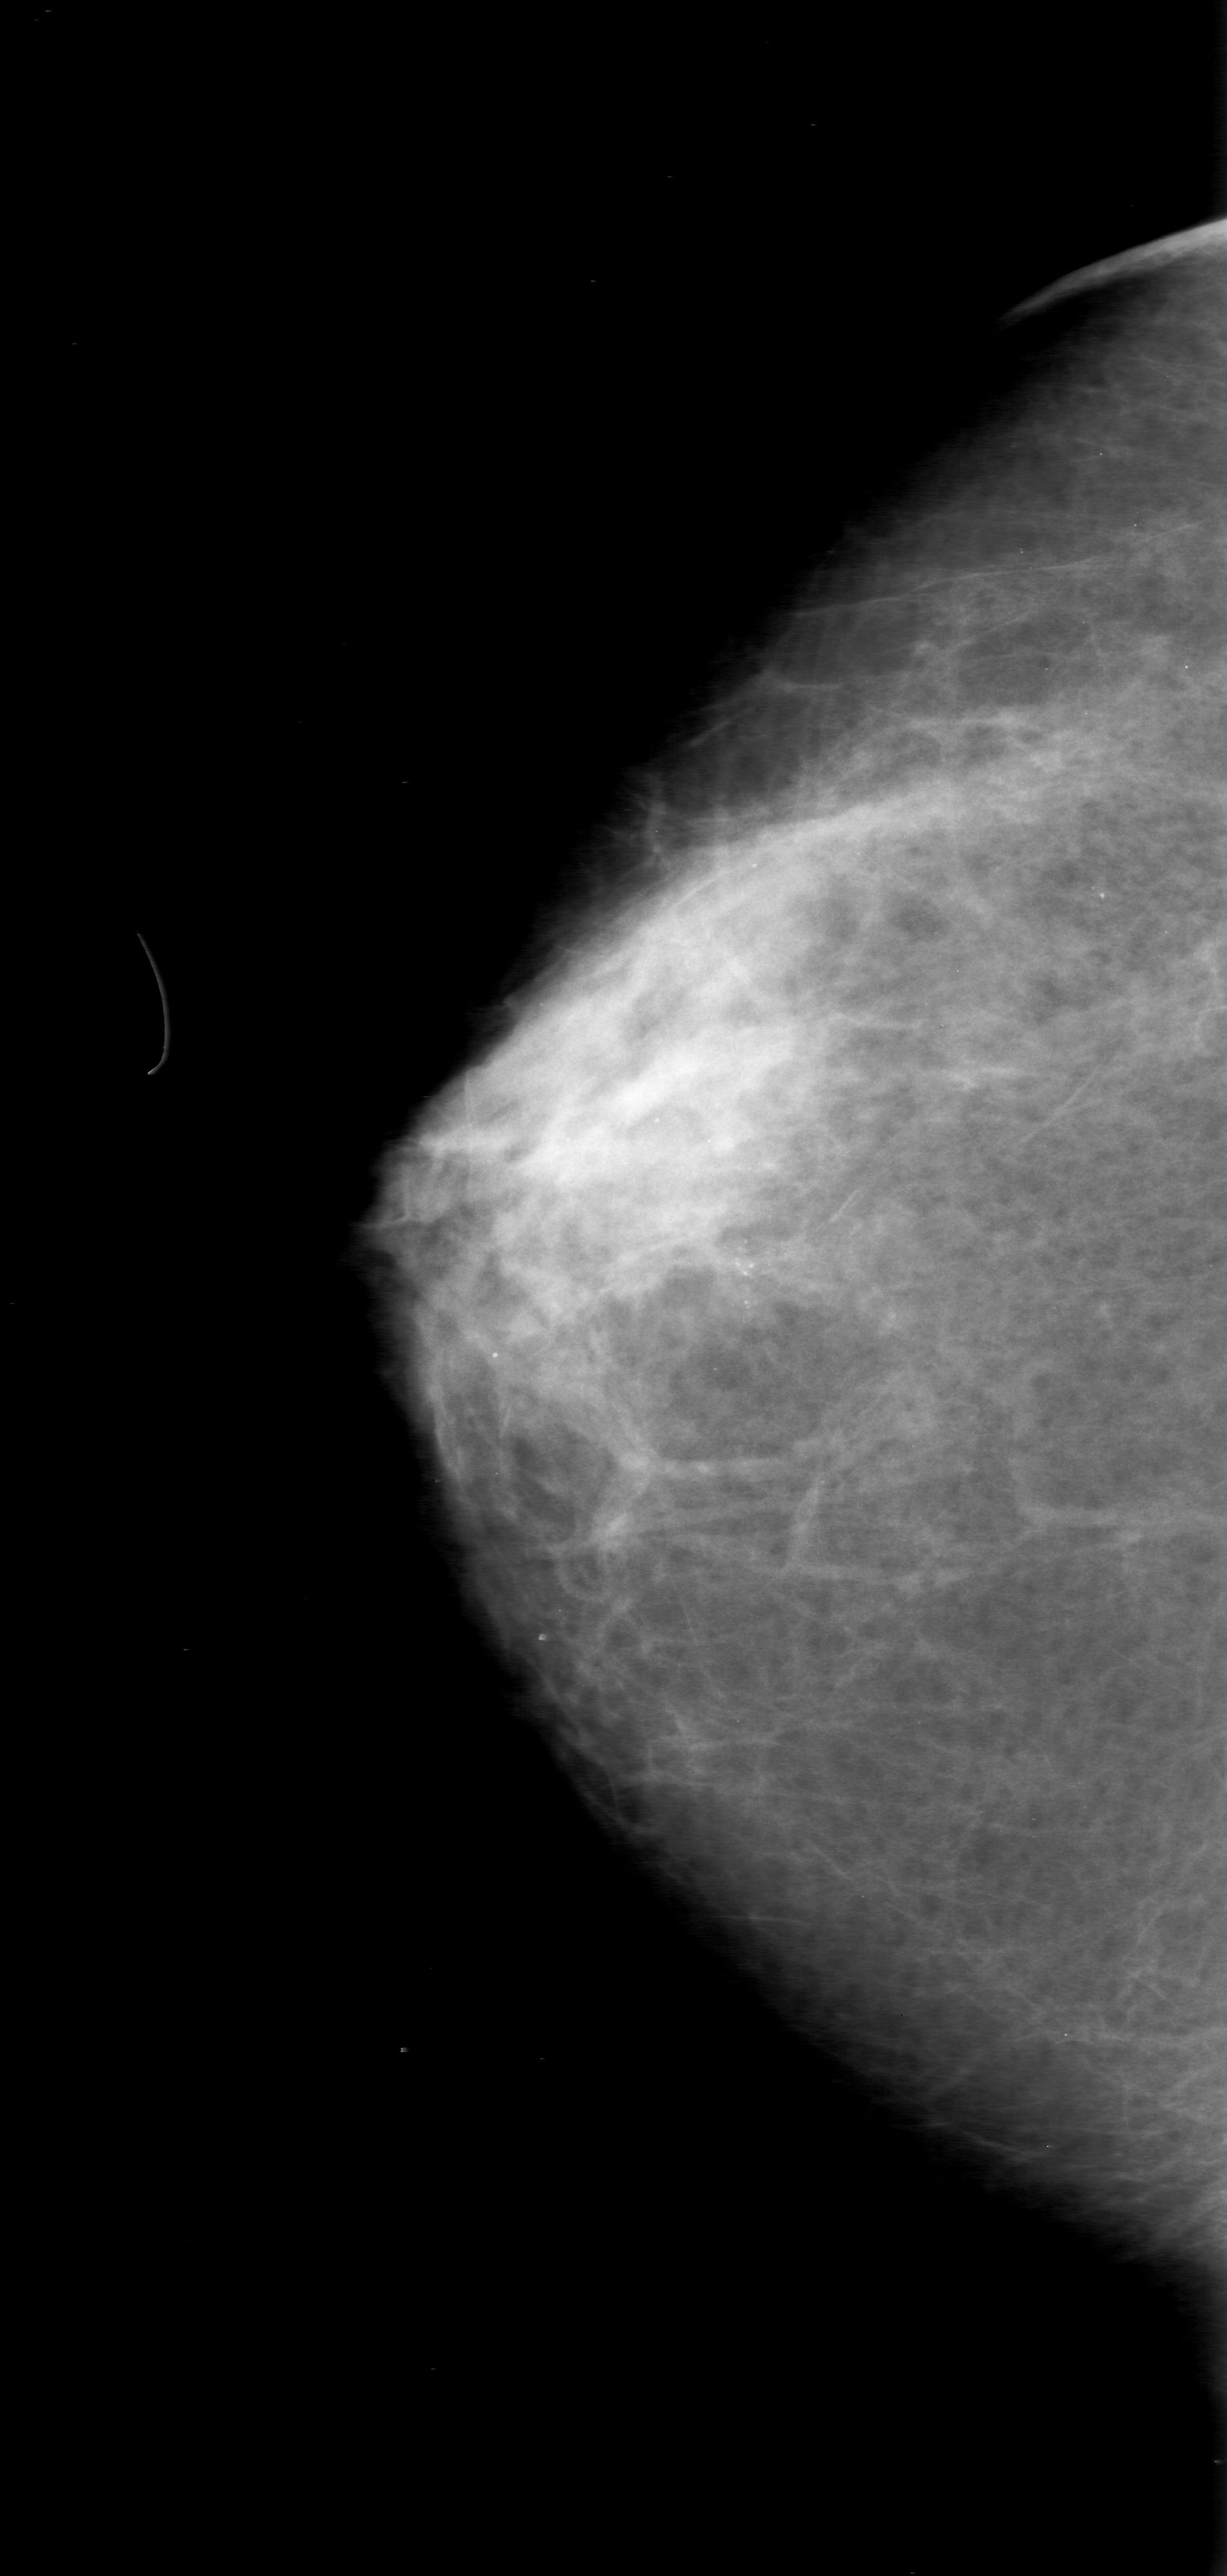
Mammogram (digitized film). Right breast. CC view. Breast composition: scattered fibroglandular densities (BI-RADS density category 2 of 4). 1227 × 2576 image matrix.
Expert-marked regions of interest on this image (one box per marked abnormality):
- calcifications, morphology pleomorphic, distribution clustered; BI-RADS assessment category 0 (incomplete: needs additional imaging); subtlety rating 4 on a 1 (subtle) to 5 (obvious) scale; pathology (as recorded): malignant: bounding box [x1, y1, x2, y2] px = [618, 1152, 851, 1368]